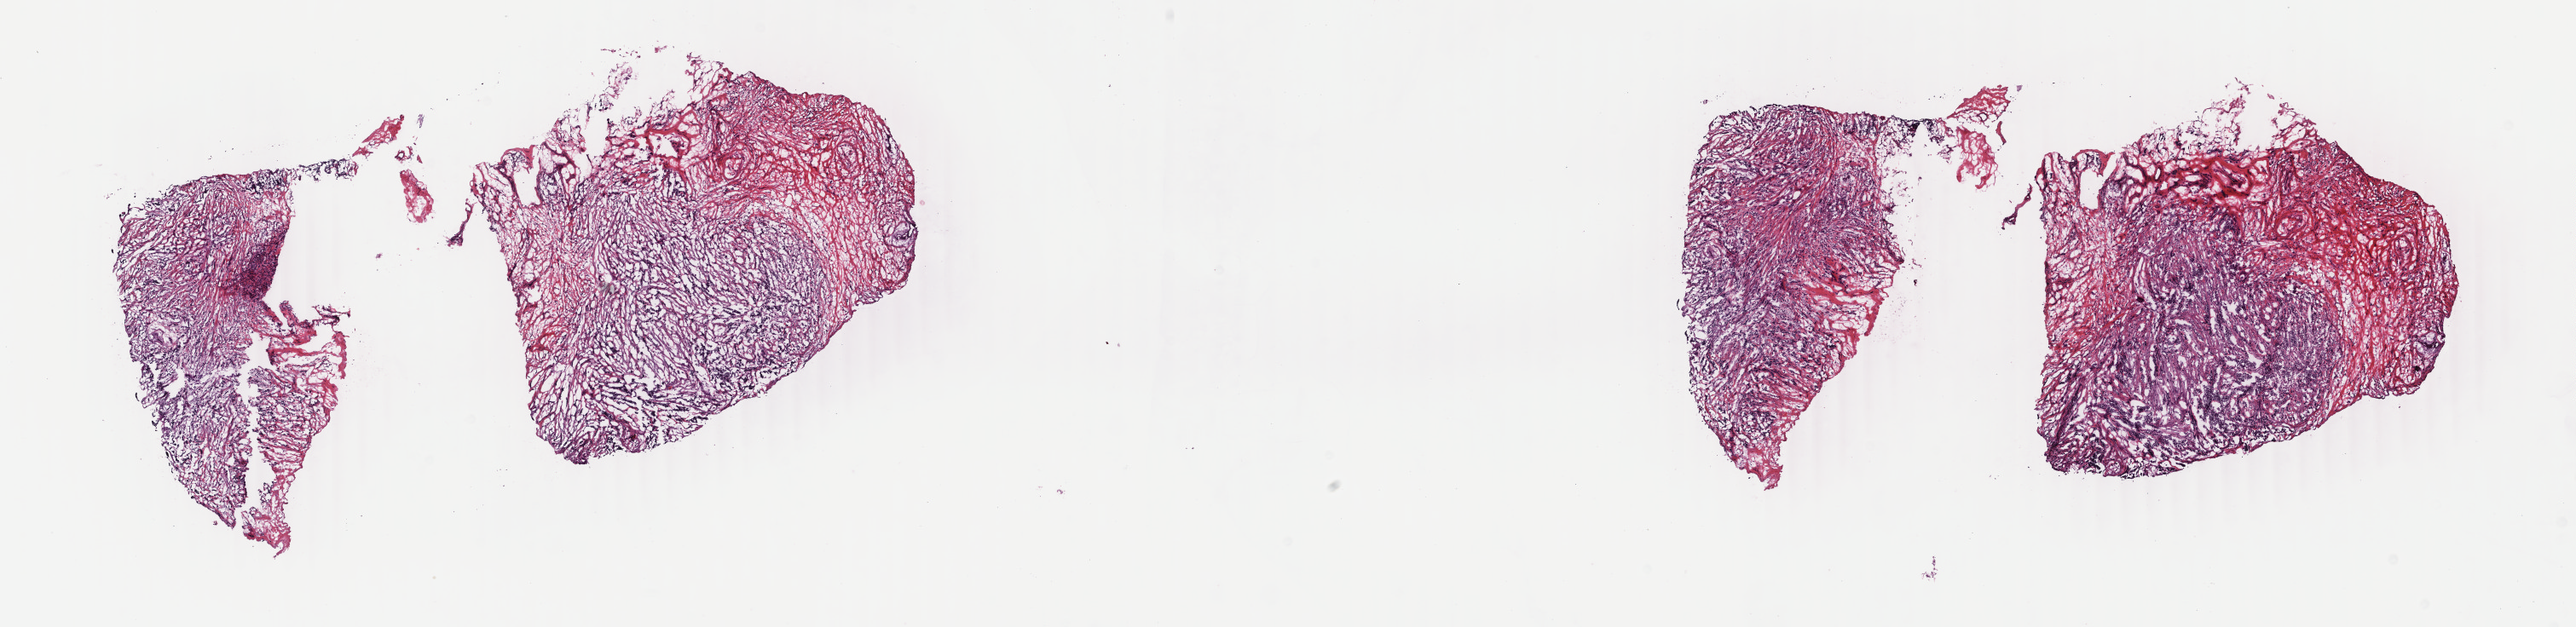
Digitized H&E tissue section (whole slide) — whole scanned area (about 24.0 x 5.9 mm, slide scanned at 40x) shown as a low-resolution overview, frozen section from the top of the tissue portion, primary tumour sample from the breast. Female patient; age at initial diagnosis 60 years. Slide review estimates, as recorded: tumour cells 72%, tumour nuclei 85%, normal cells 0%, stromal cells 28%, necrosis 0%. Inflammatory infiltration, as recorded: lymphocyte infiltration 2%, monocyte infiltration 0%, neutrophil infiltration 0%.
* pathologic diagnosis: Infiltrating duct carcinoma, NOS
* AJCC pathologic stage: IA